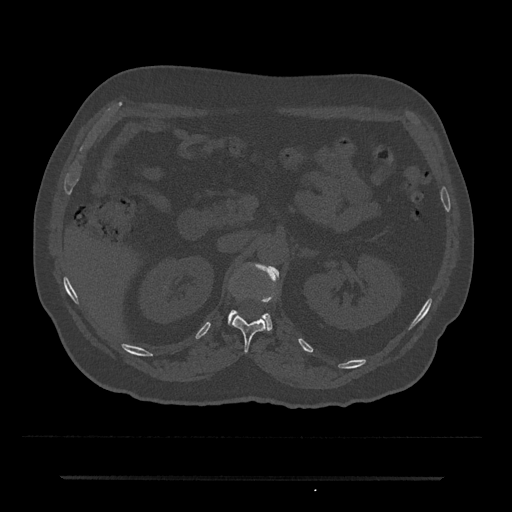
CT including the spine, one axial slice. Position 107 of 797 along the scan axis. Reconstruction kernel Br40s/3. 120 kVp. Bone window (W 1800 / L 400 HU). 0.5 mm slice thickness. 512 × 512 image matrix. Male patient, age 69 years. Case-level facts recorded for this patient, not image findings: primary cancer: prostate.
Structures marked on this image (semi-automatically segmented with operator editing):
- L1 vertebra: bounding box (x1, y1, x2, y2) in pixels: (228, 265, 279, 330)
- T12 vertebra: (232, 315, 267, 351)